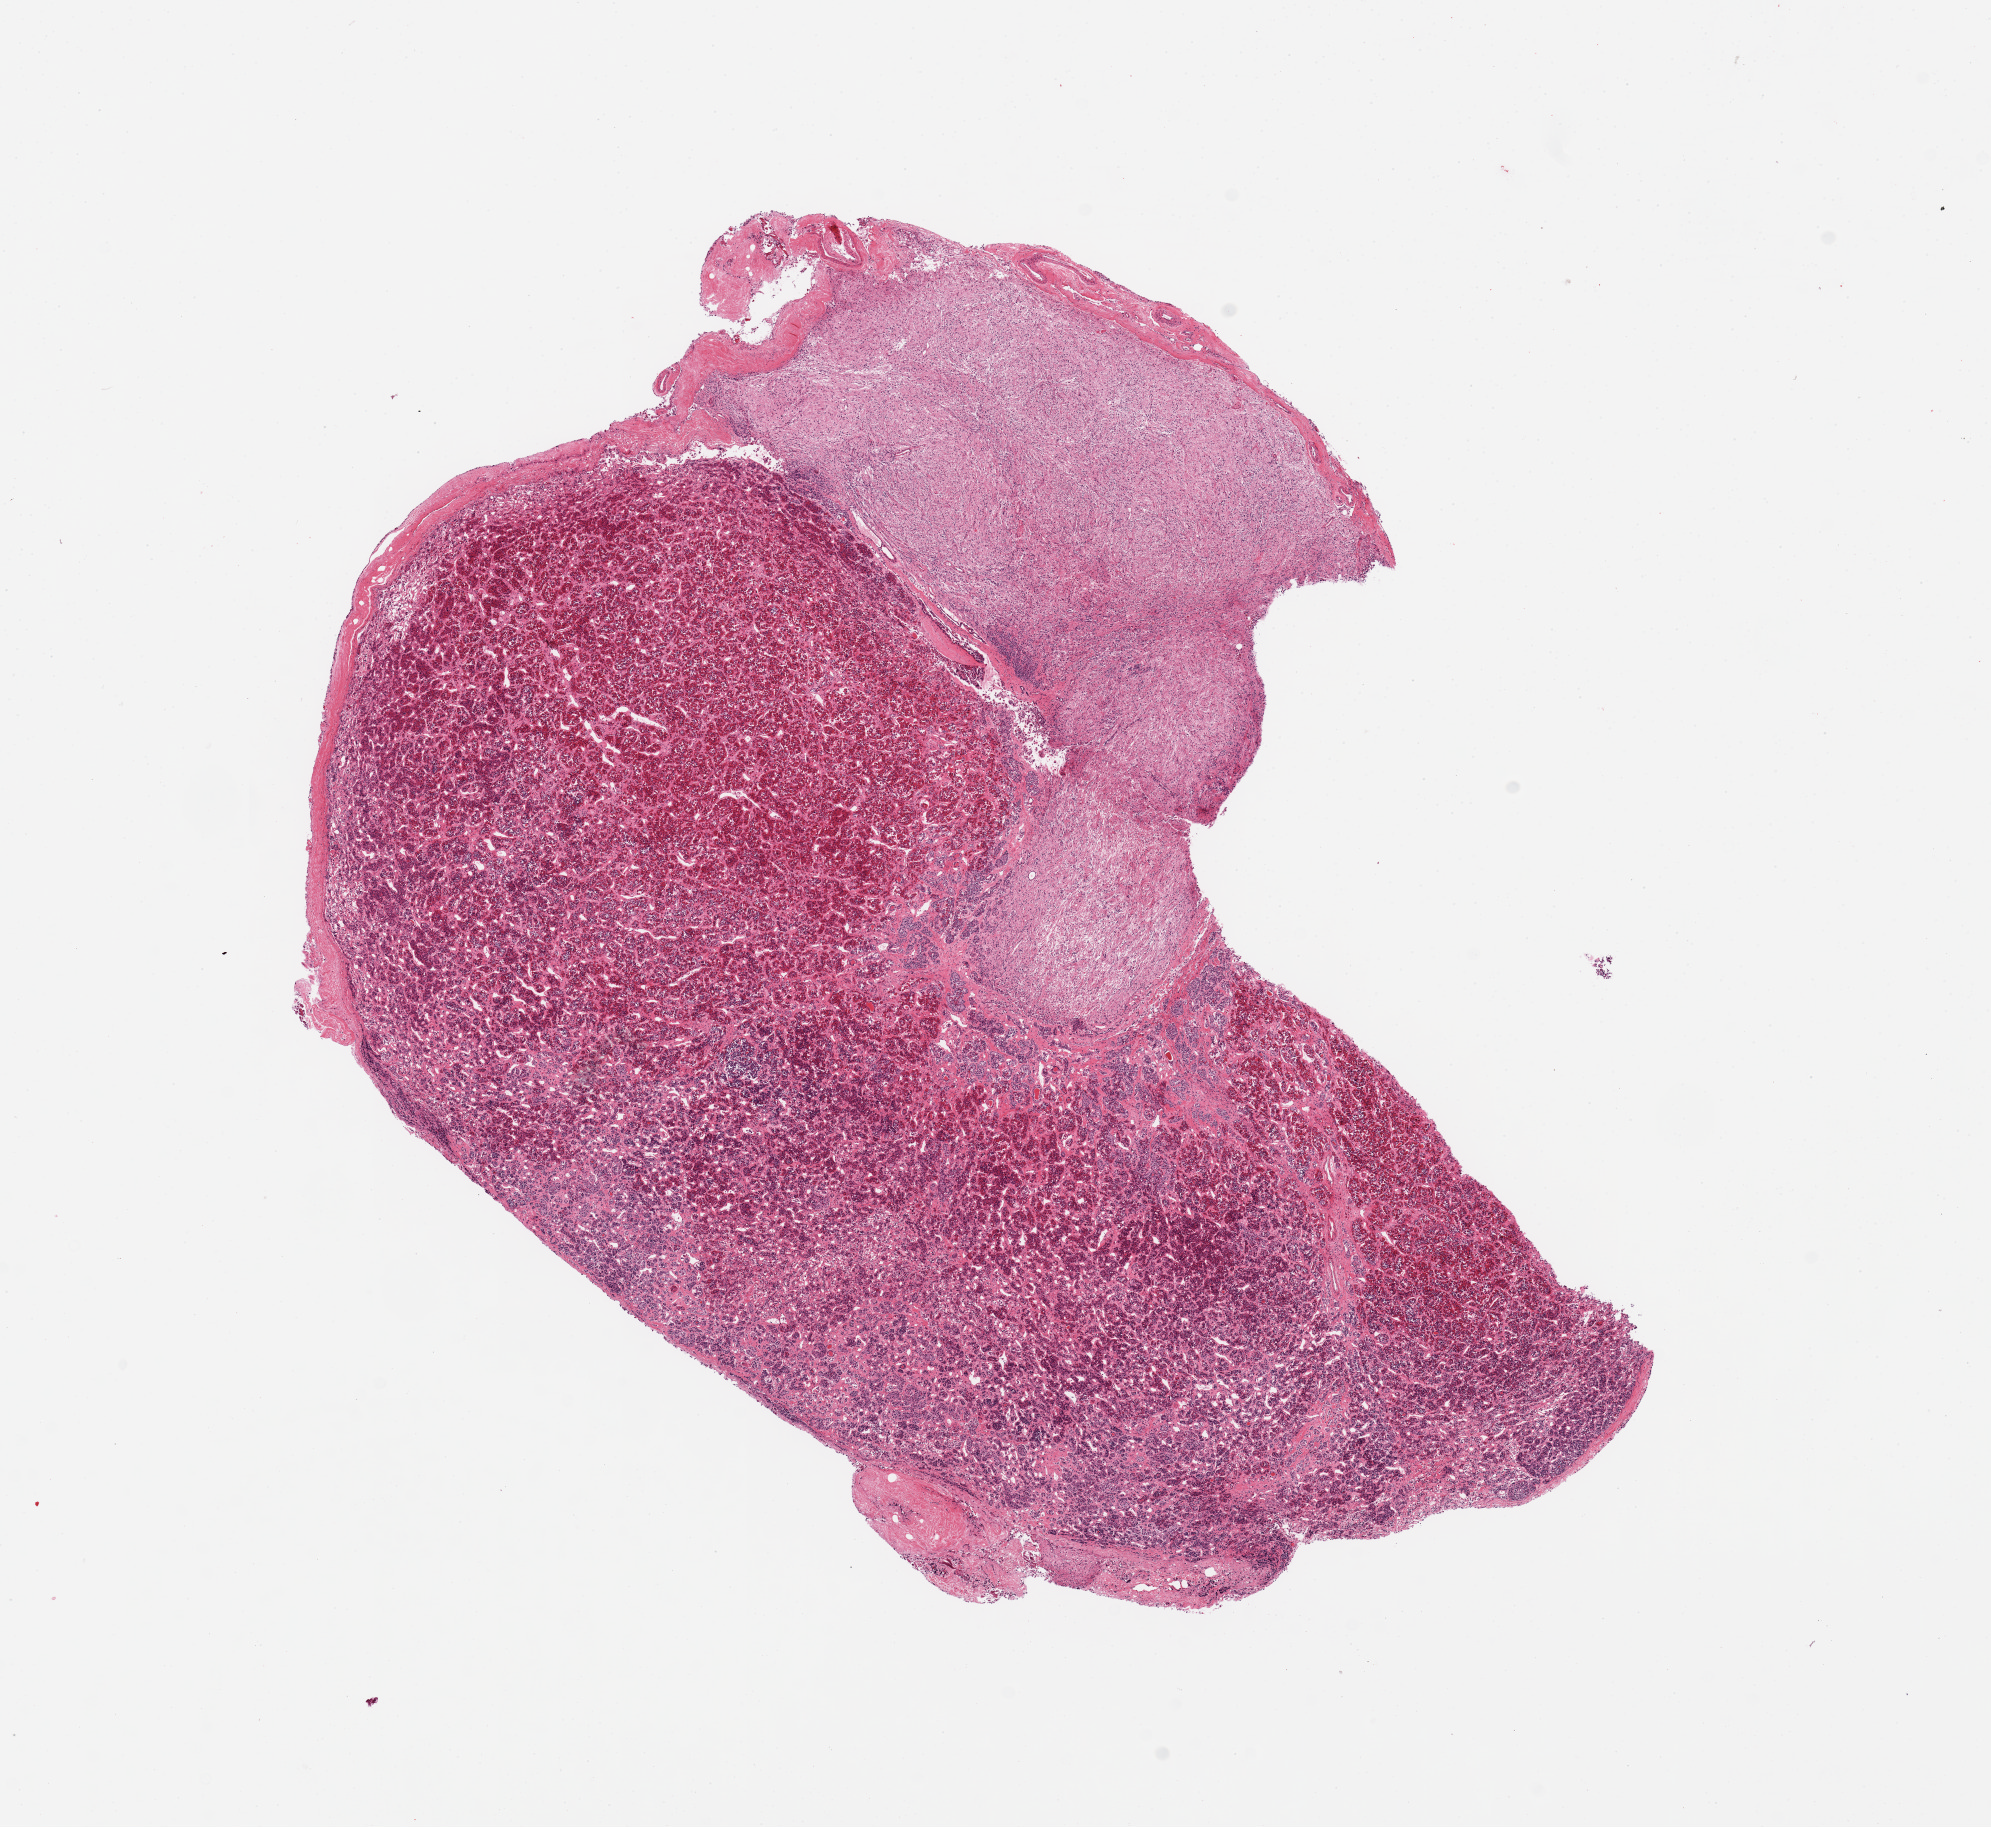
Haematoxylin and eosin whole-slide image, brightfield — shown as a low-resolution overview of the whole scanned area (about 15.8 x 14.5 mm, acquisition: 20x scan); PAXgene-fixed, paraffin-embedded tissue; sampled site (target tissue): pituitary; tissue donor sample. Male donor.
Pathologist's review note for this sample: 1 piece, 60% adenohypophysis, 40 % neurohypophysis.